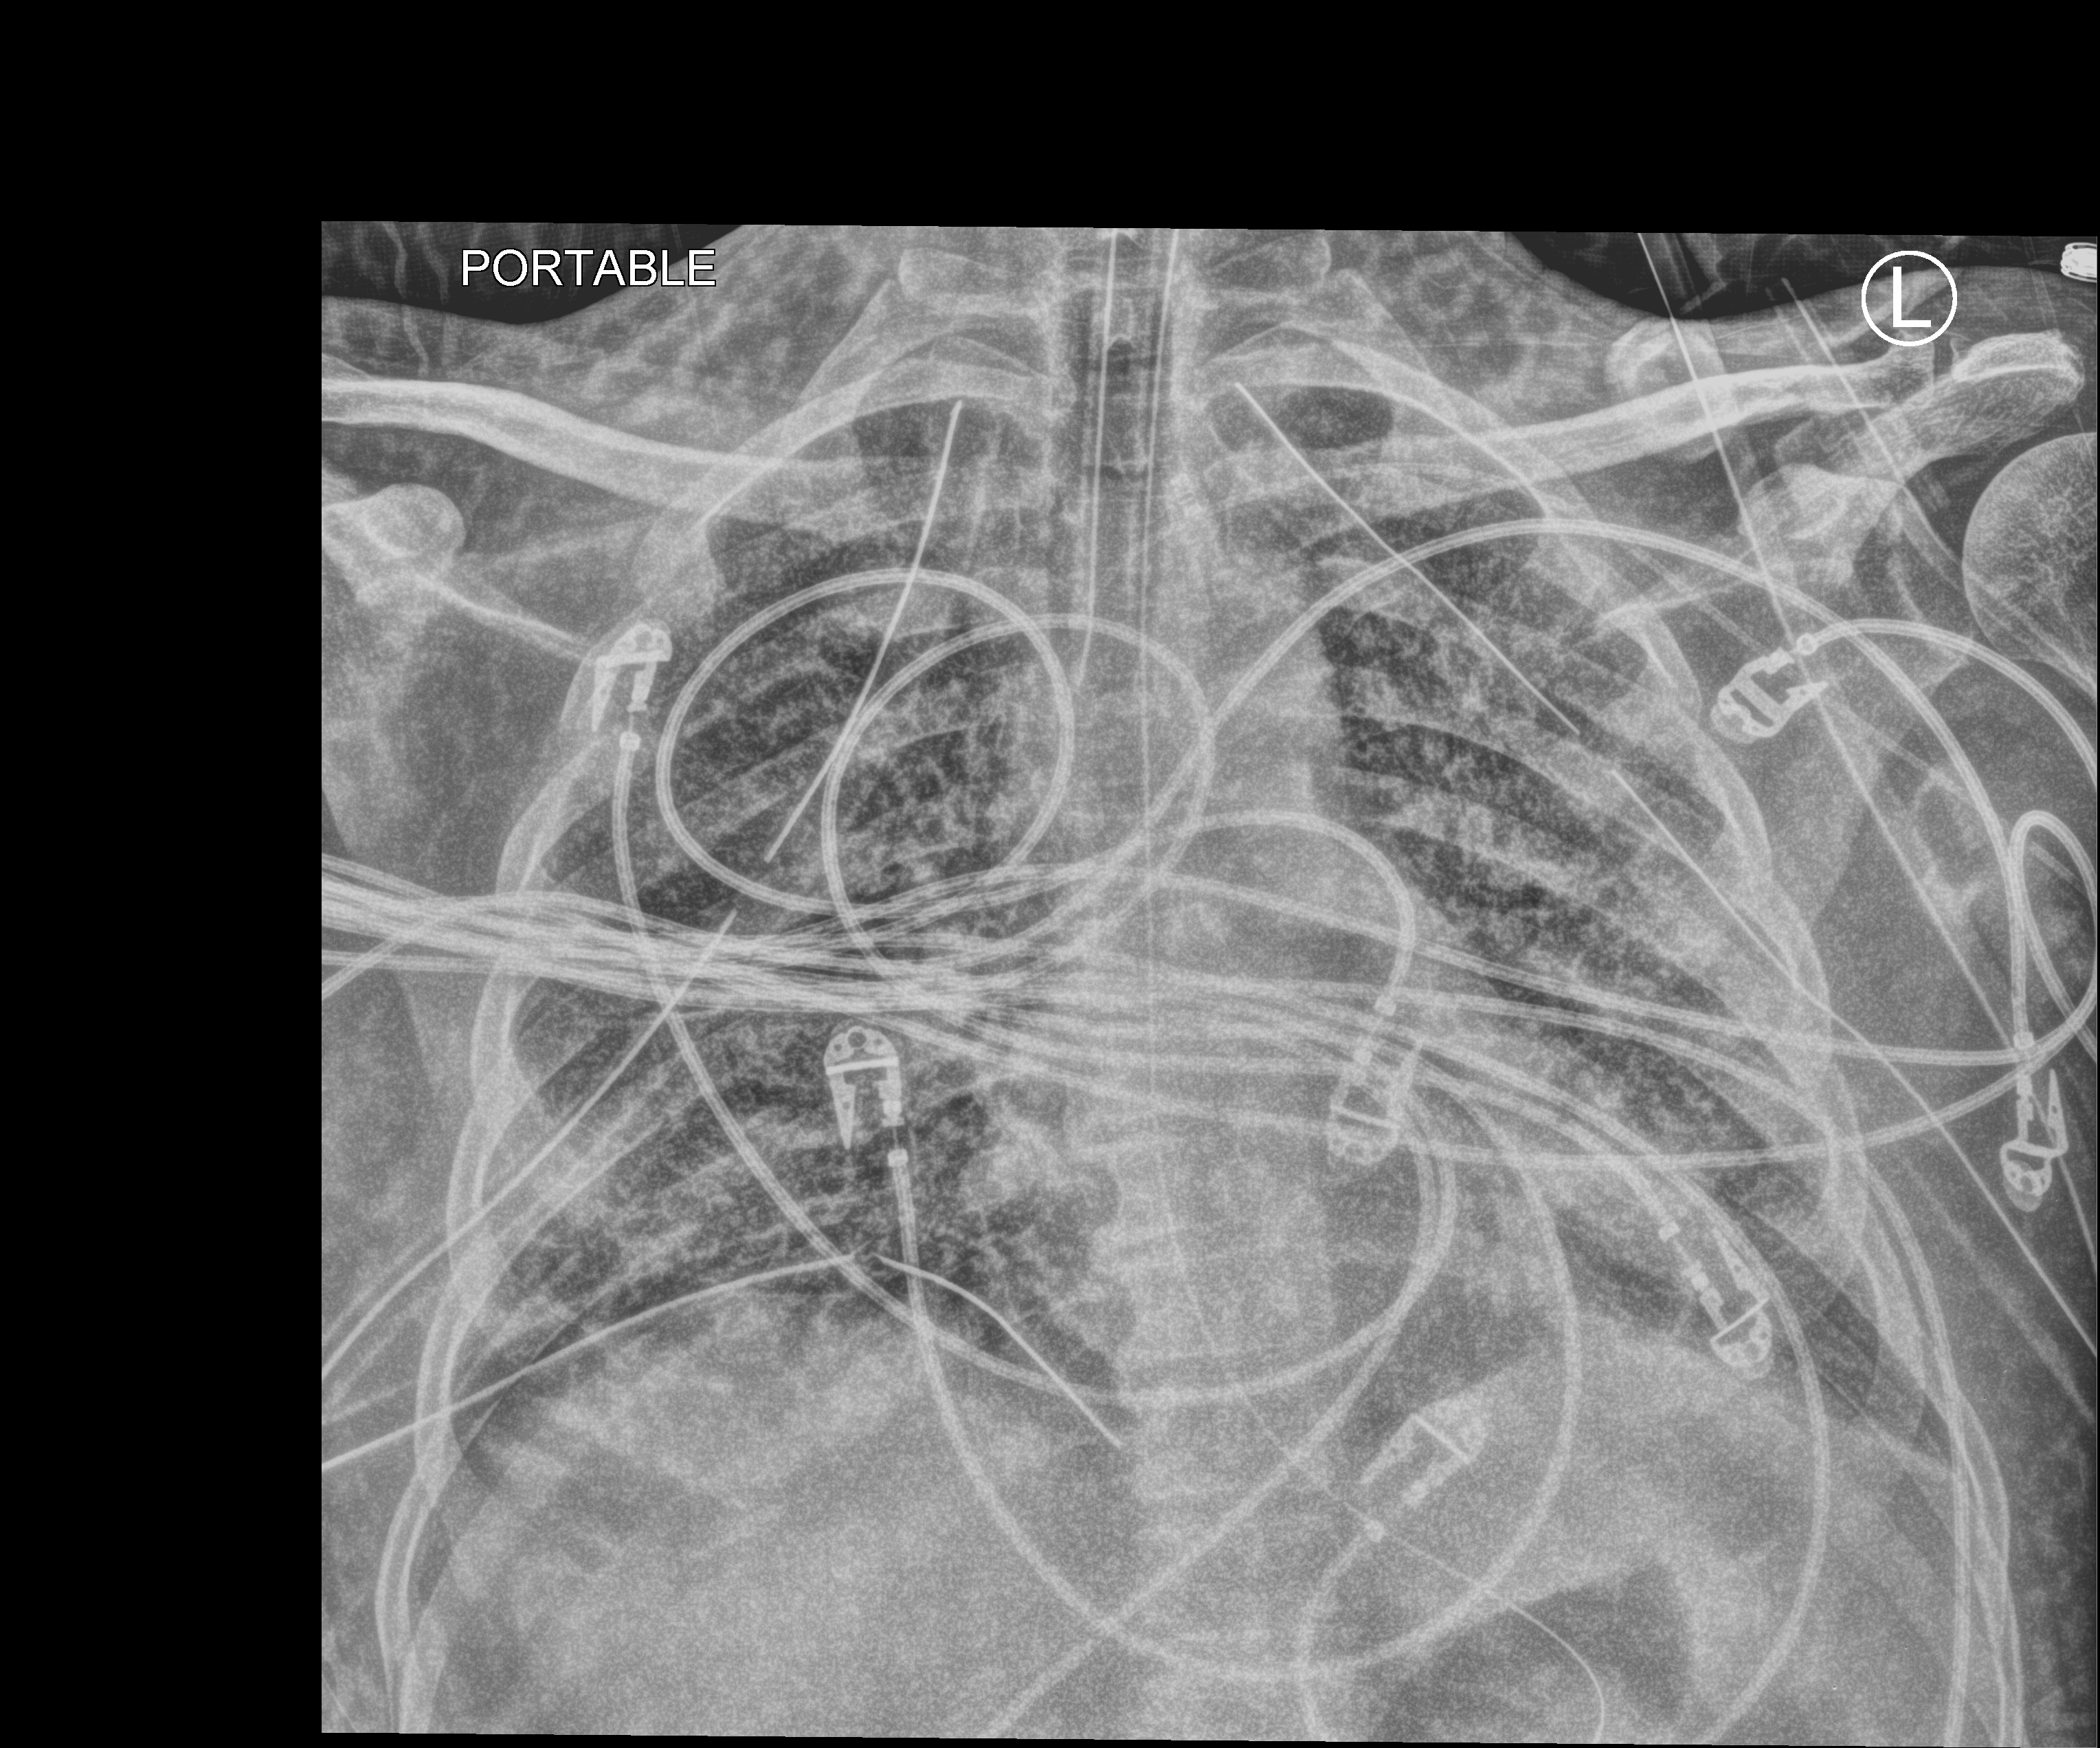
Bedside chest radiograph (computed radiography), anteroposterior (AP) projection. Male patient hospitalised with COVID-19, age 18–59 years.
From the hospital-stay record, not from the radiograph (when in the stay this image was taken is not recorded): hypertension (admission record): yes.